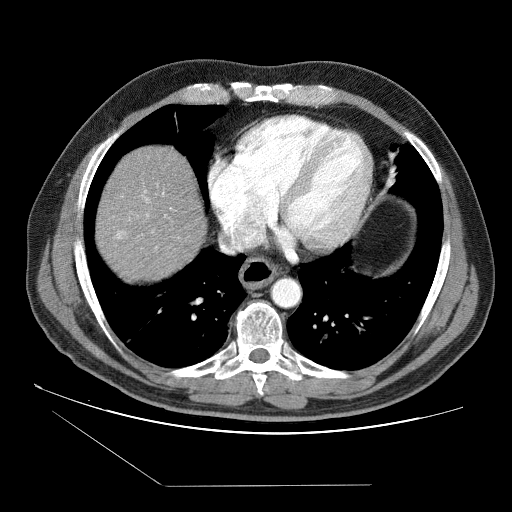
Contrast-enhanced abdominal CT (liver protocol), one axial slice; 120 kVp; soft-tissue window (W 400 / L 40 HU); 2.5 mm slice thickness; 512 × 512 image matrix. Case-level facts recorded for this patient, not image findings: diagnosis: hepatocellular carcinoma (patient treated with transarterial chemoembolisation; whether this scan precedes or follows treatment is not stated here); TNM stage (as recorded): Stage-II; Child-Pugh class: B; tumour differentiation: no biopsy; tumour nodularity: multinodular.
Annotated regions visible in this slice (semi-automatically segmented with operator editing):
- liver parenchyma outside the tumour (the mass and vessels are separate outlines, so this box may not span the whole liver): box from (x=96, y=146) to (x=206, y=278) px
- liver vessels: (x=117, y=215)–(x=166, y=238)